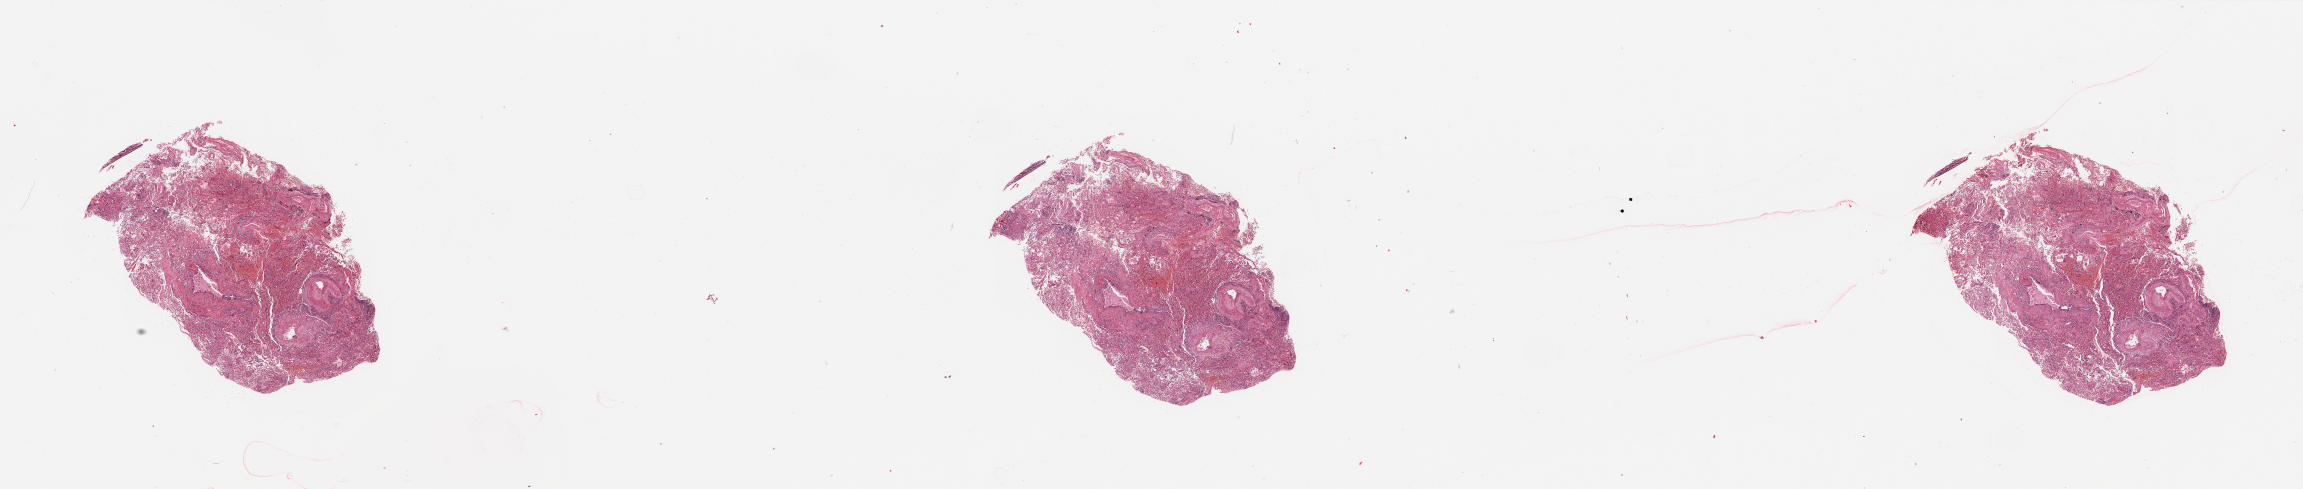
Digitized H&E tissue section (whole slide) — a low-resolution overview of the entire scanned area, about 36.4 x 7.7 mm (acquisition: 20x scan), normal (non-tumour) tissue sample, sampled site: lung. 73-year-old male patient.
This section: normal (non-tumour) tissue from the same patient. Patient diagnosis: Squamous cell carcinoma, NOS.